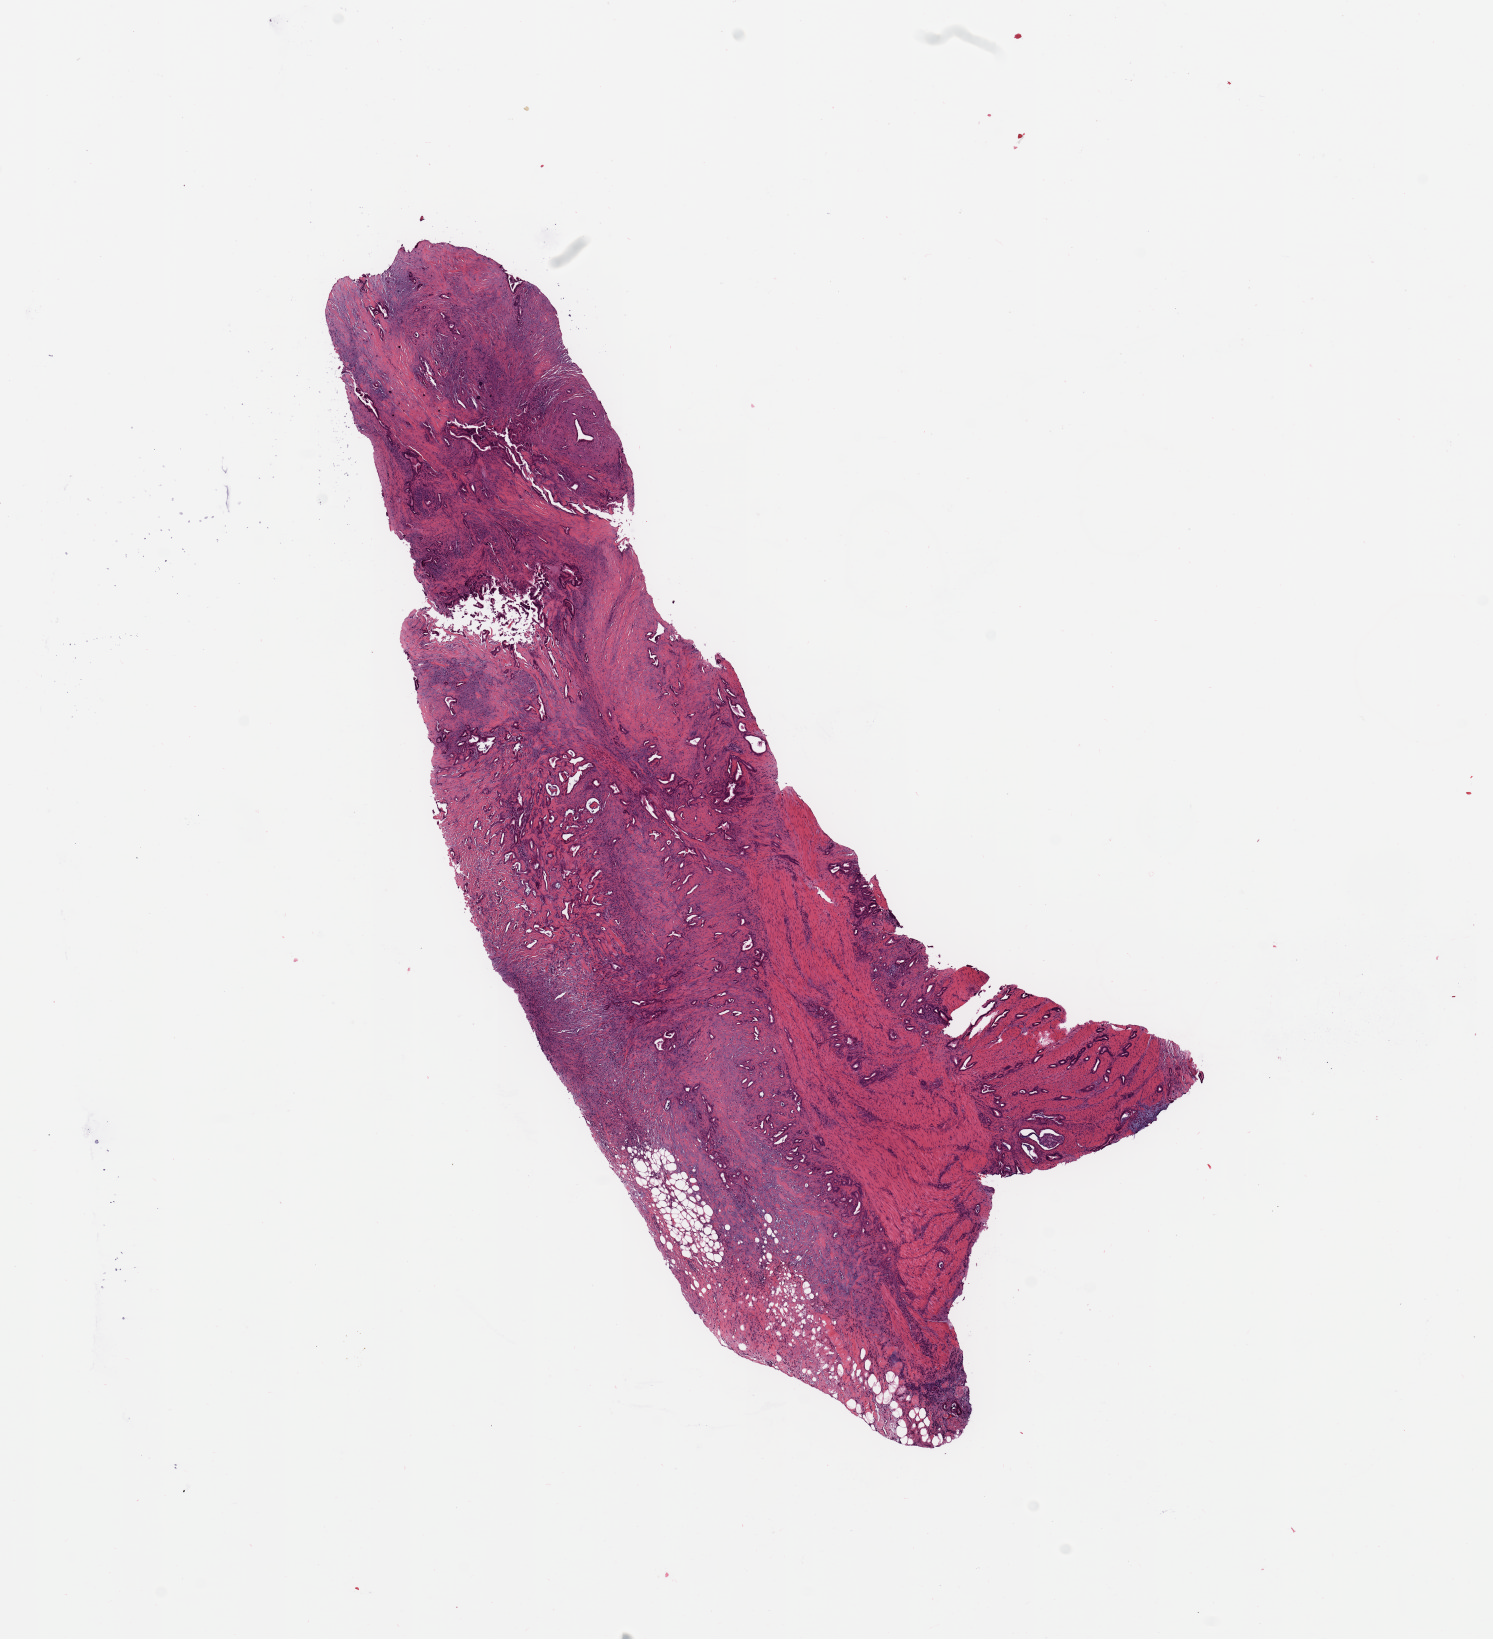
Whole-slide histology image, H&E — a low-resolution overview of the entire scanned area, about 11.8 x 13.0 mm. Pancreas, tissue type not recorded.
Patient diagnosis (cohort enrolment): ductal adenocarcinoma (pancreas).